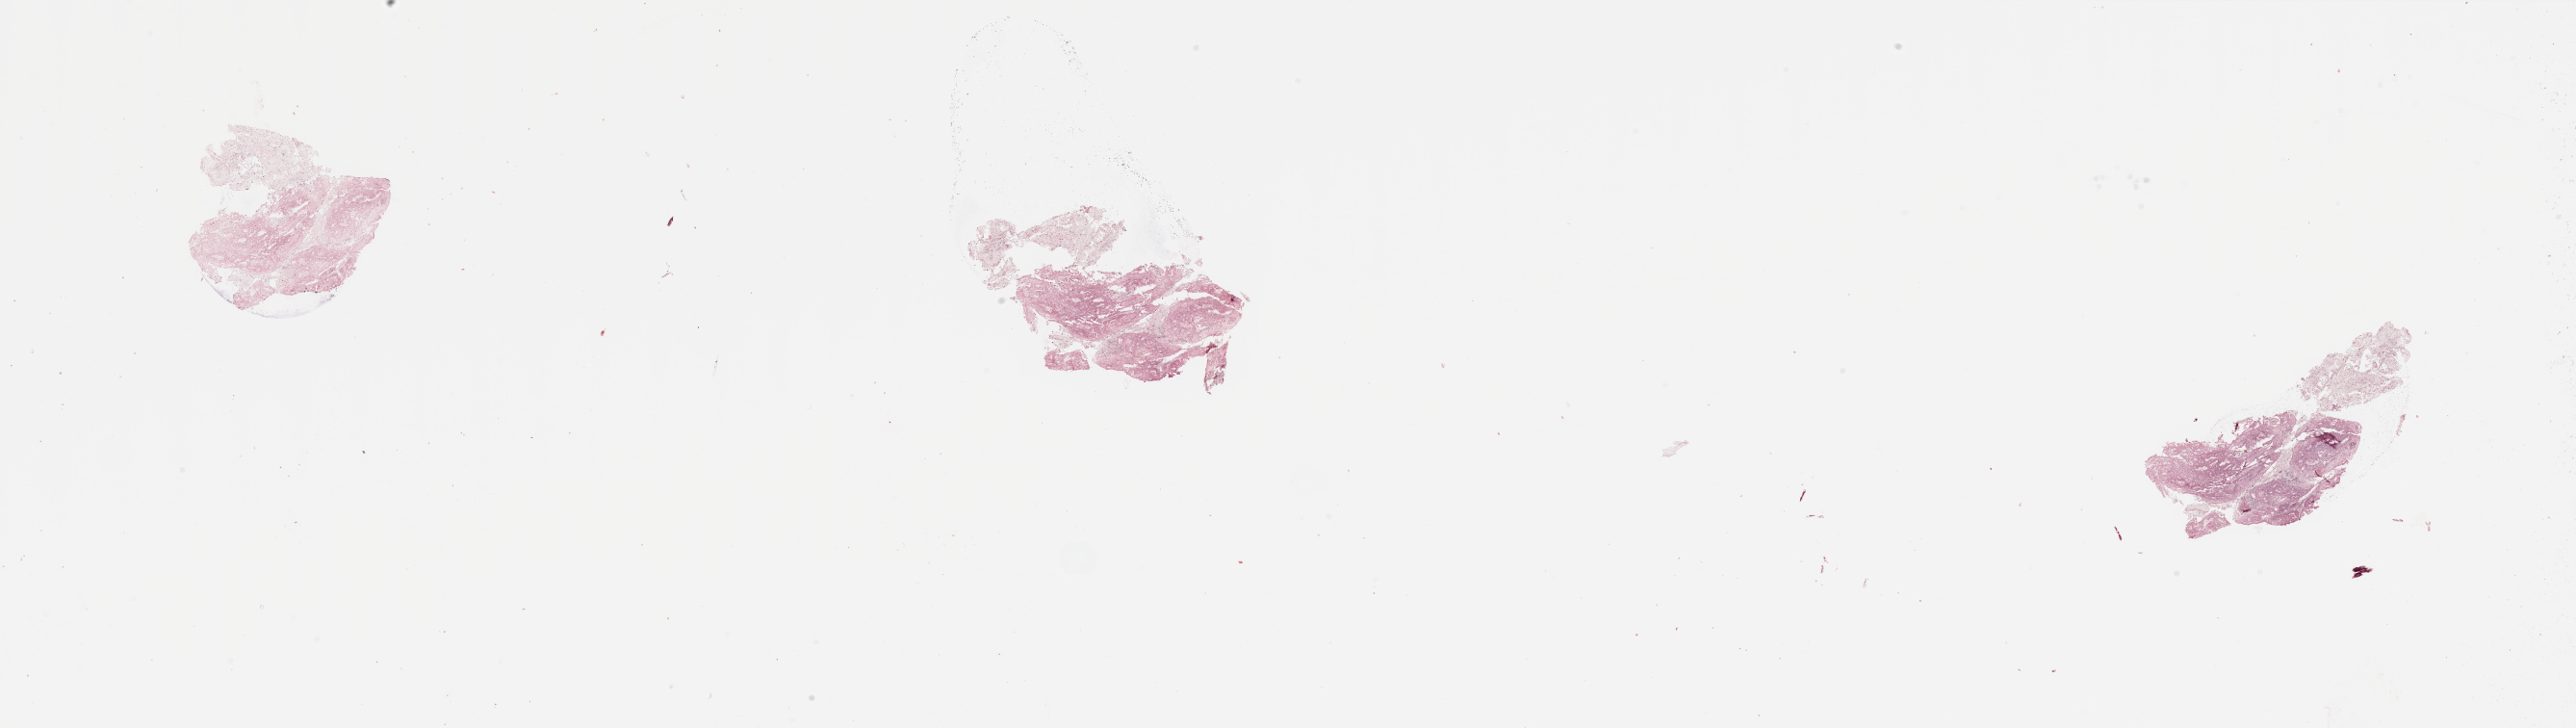
Digitized H&E tissue section (whole slide), a low-resolution overview of the entire scanned area, about 42.3 x 12.0 mm, tumour tissue sample, sampled site: uterus. Patient: female, age 80 years. Histologic grade: G2 (moderately differentiated). Composition of this section per pathologist review: tumour nuclei 80%, necrosis 5%.
- primary tumour site (as recorded): anterior endometrium
- AJCC pathologic stage: I
- diagnosis: Endometrioid adenocarcinoma, NOS